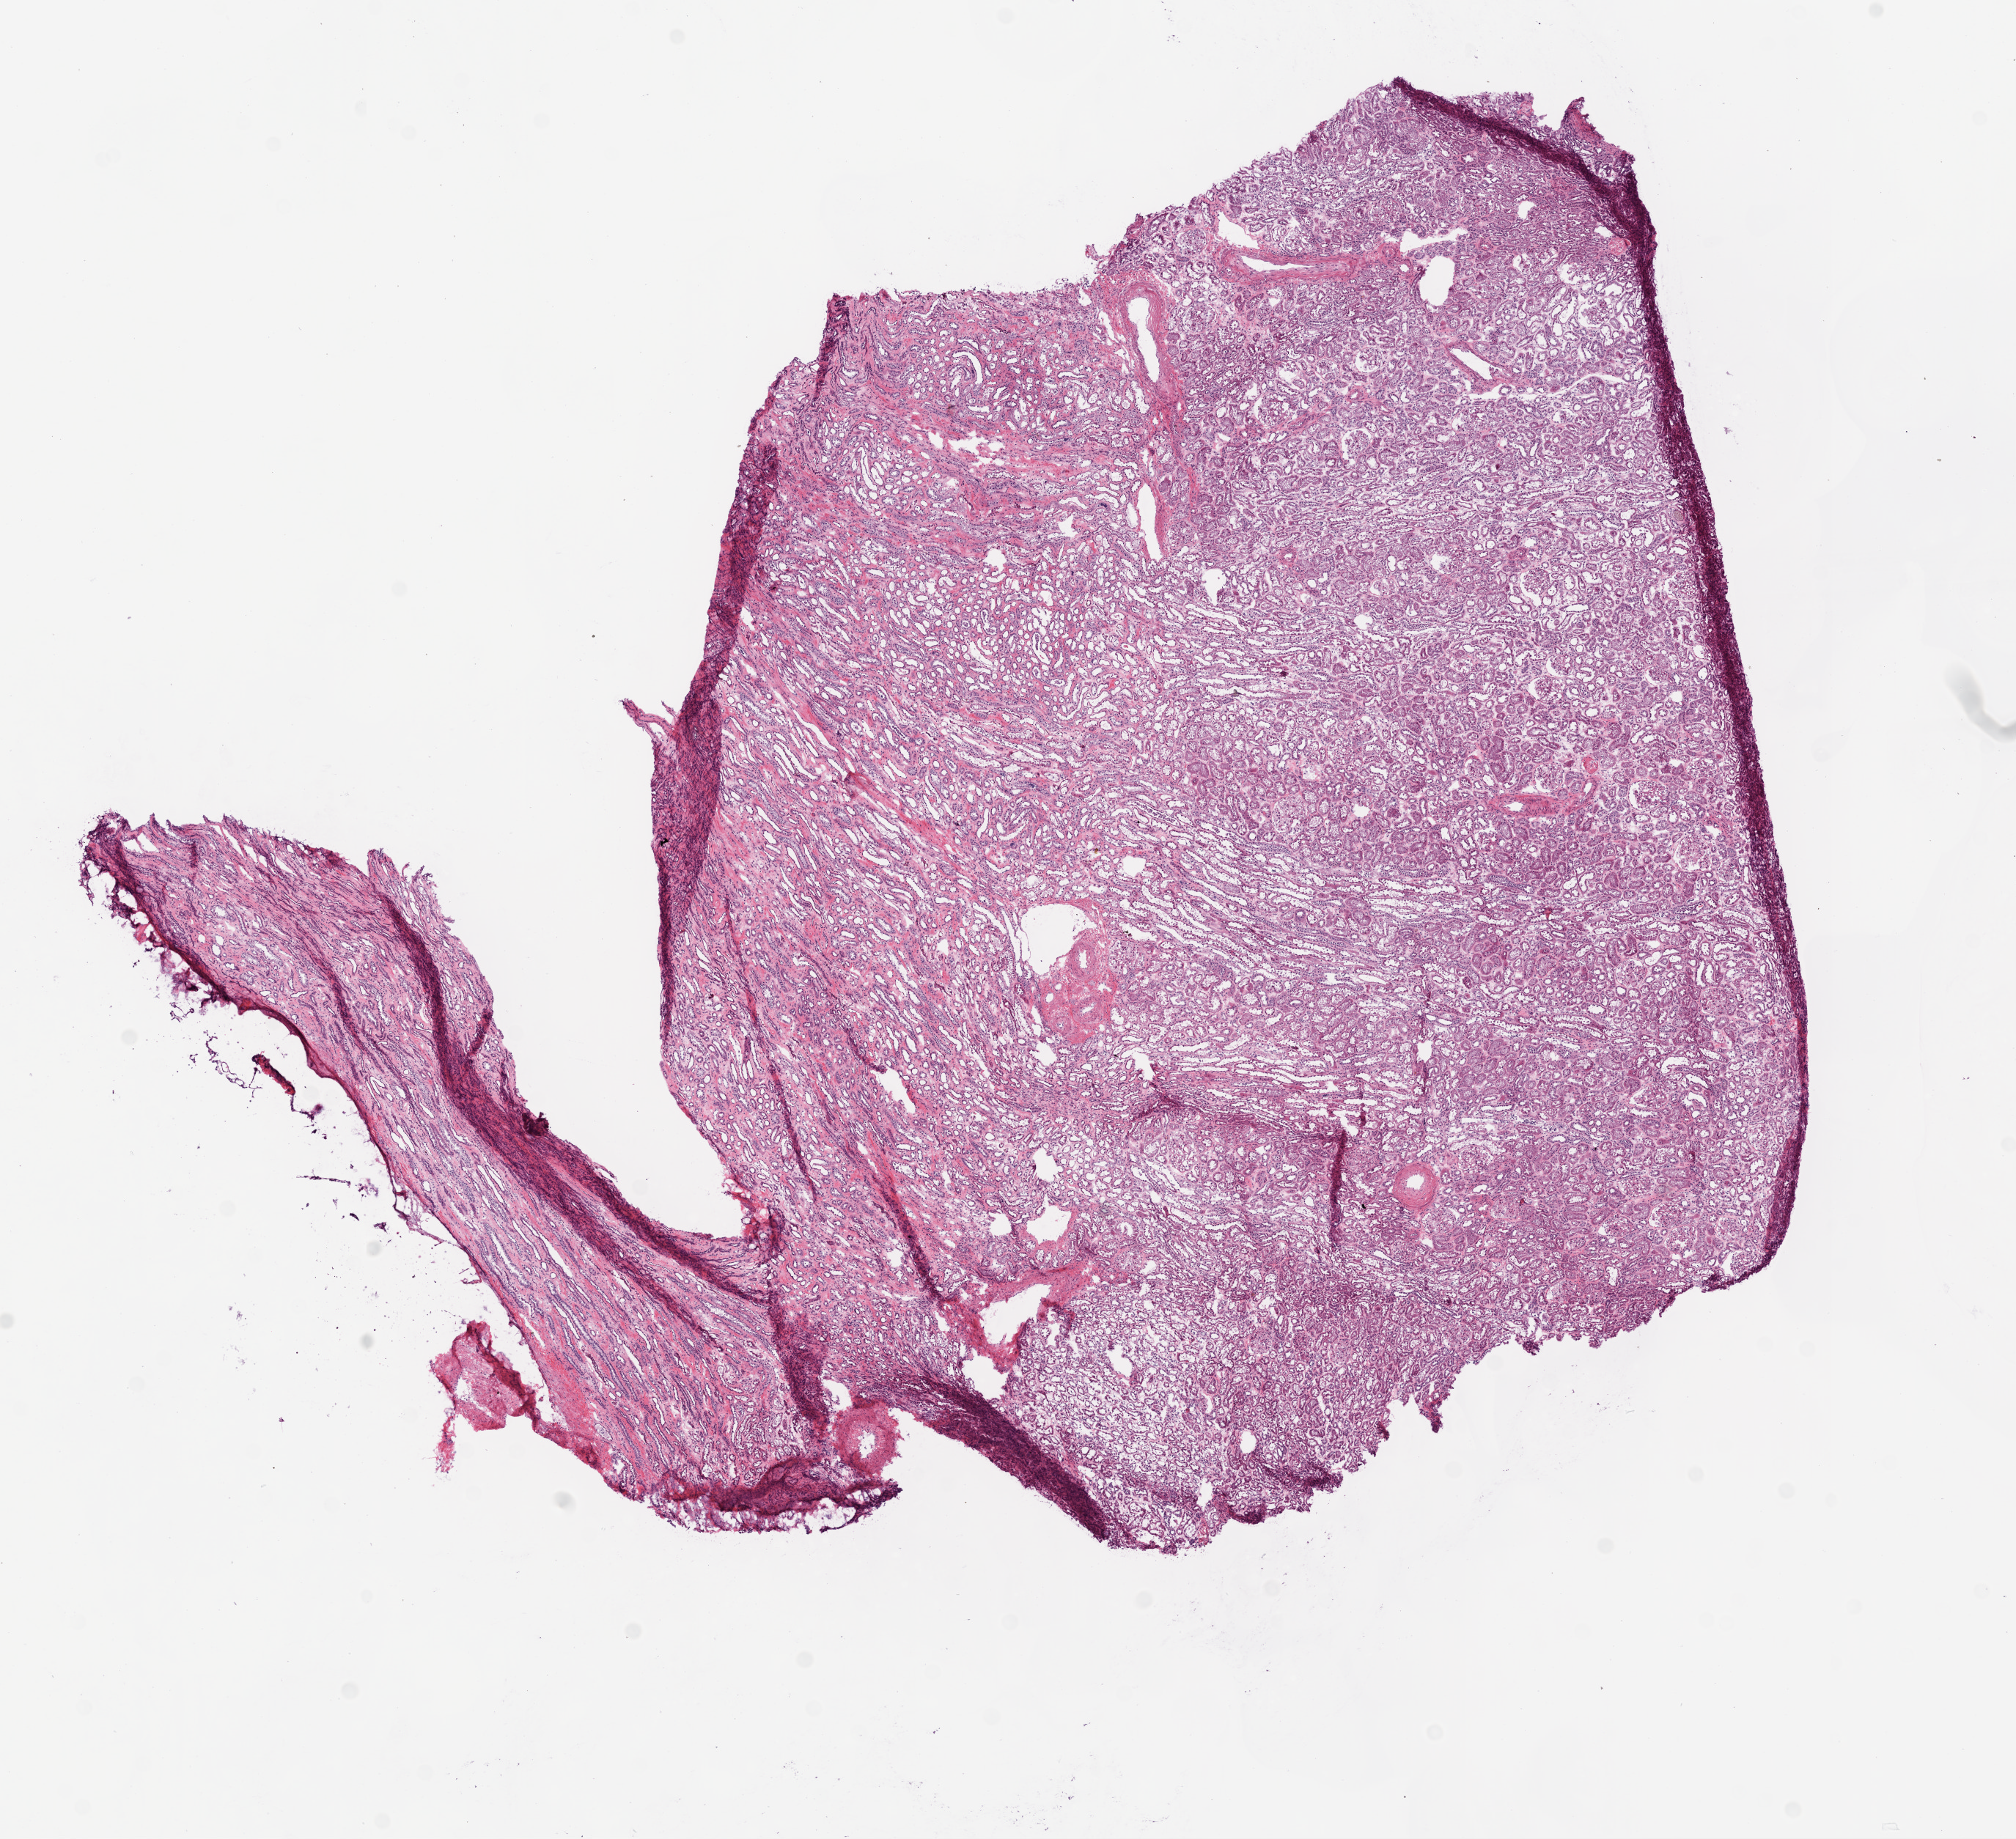
Digitized Hematoxylin and eosin (H&E) stained tissue section (whole slide) — shown as a low-resolution overview of the whole scanned area (about 11.0 x 10.1 mm, acquisition: 20x scan); frozen section from the bottom of the tissue portion; sample: solid tissue normal (non-tumour tissue), kidney. Patient: male, age at initial diagnosis 57 years.
This section: solid tissue normal (non-tumour) sample from the same patient. Patient diagnosis: Clear cell adenocarcinoma, NOS.